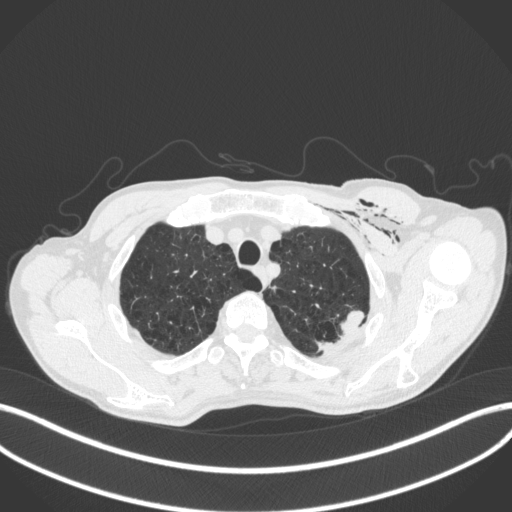
Chest CT, one axial slice; slice 354 of 416 in the series (ordered by position); reconstruction kernel B31f; 120 kVp; lung window (W 1500 / L -600 HU); 1 mm slice thickness; 512 × 512 image matrix, field of view 400 × 400 mm. Male patient, age 58 years. Case-level facts recorded for this patient, not image findings: clinical TNM (as recorded): T3 N0 M0.
Annotated regions visible in this slice (bounding box drawn by a radiologist):
- lung tumour (recorded histology: adenocarcinoma): bounding box [x1, y1, x2, y2] px = [339, 307, 369, 335]